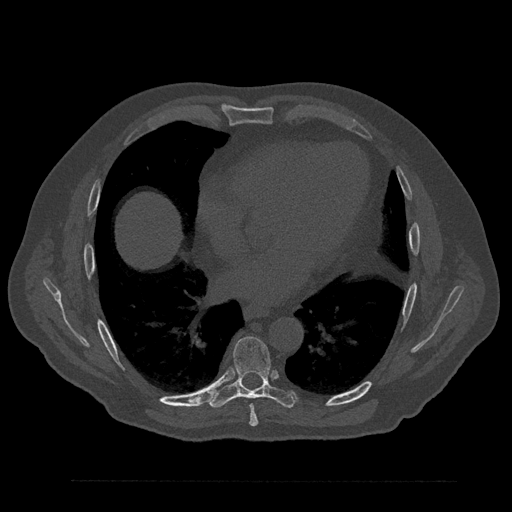
CT including the spine, one axial slice; position 465 of 797 along the scan axis; 120 kVp; bone window (W 1800 / L 400 HU); 0.5 mm slice thickness; 512 × 512 image matrix. Male patient, age 61 years. Case-level facts recorded for this patient, not image findings: primary cancer: prostate.
Annotated regions visible in this slice (semi-automatic segmentation, software-assisted and operator-edited):
- T7 vertebra: bounding box <249,404,258,426> (left, top, right, bottom; pixels)
- T8 vertebra: <208,336,296,409>